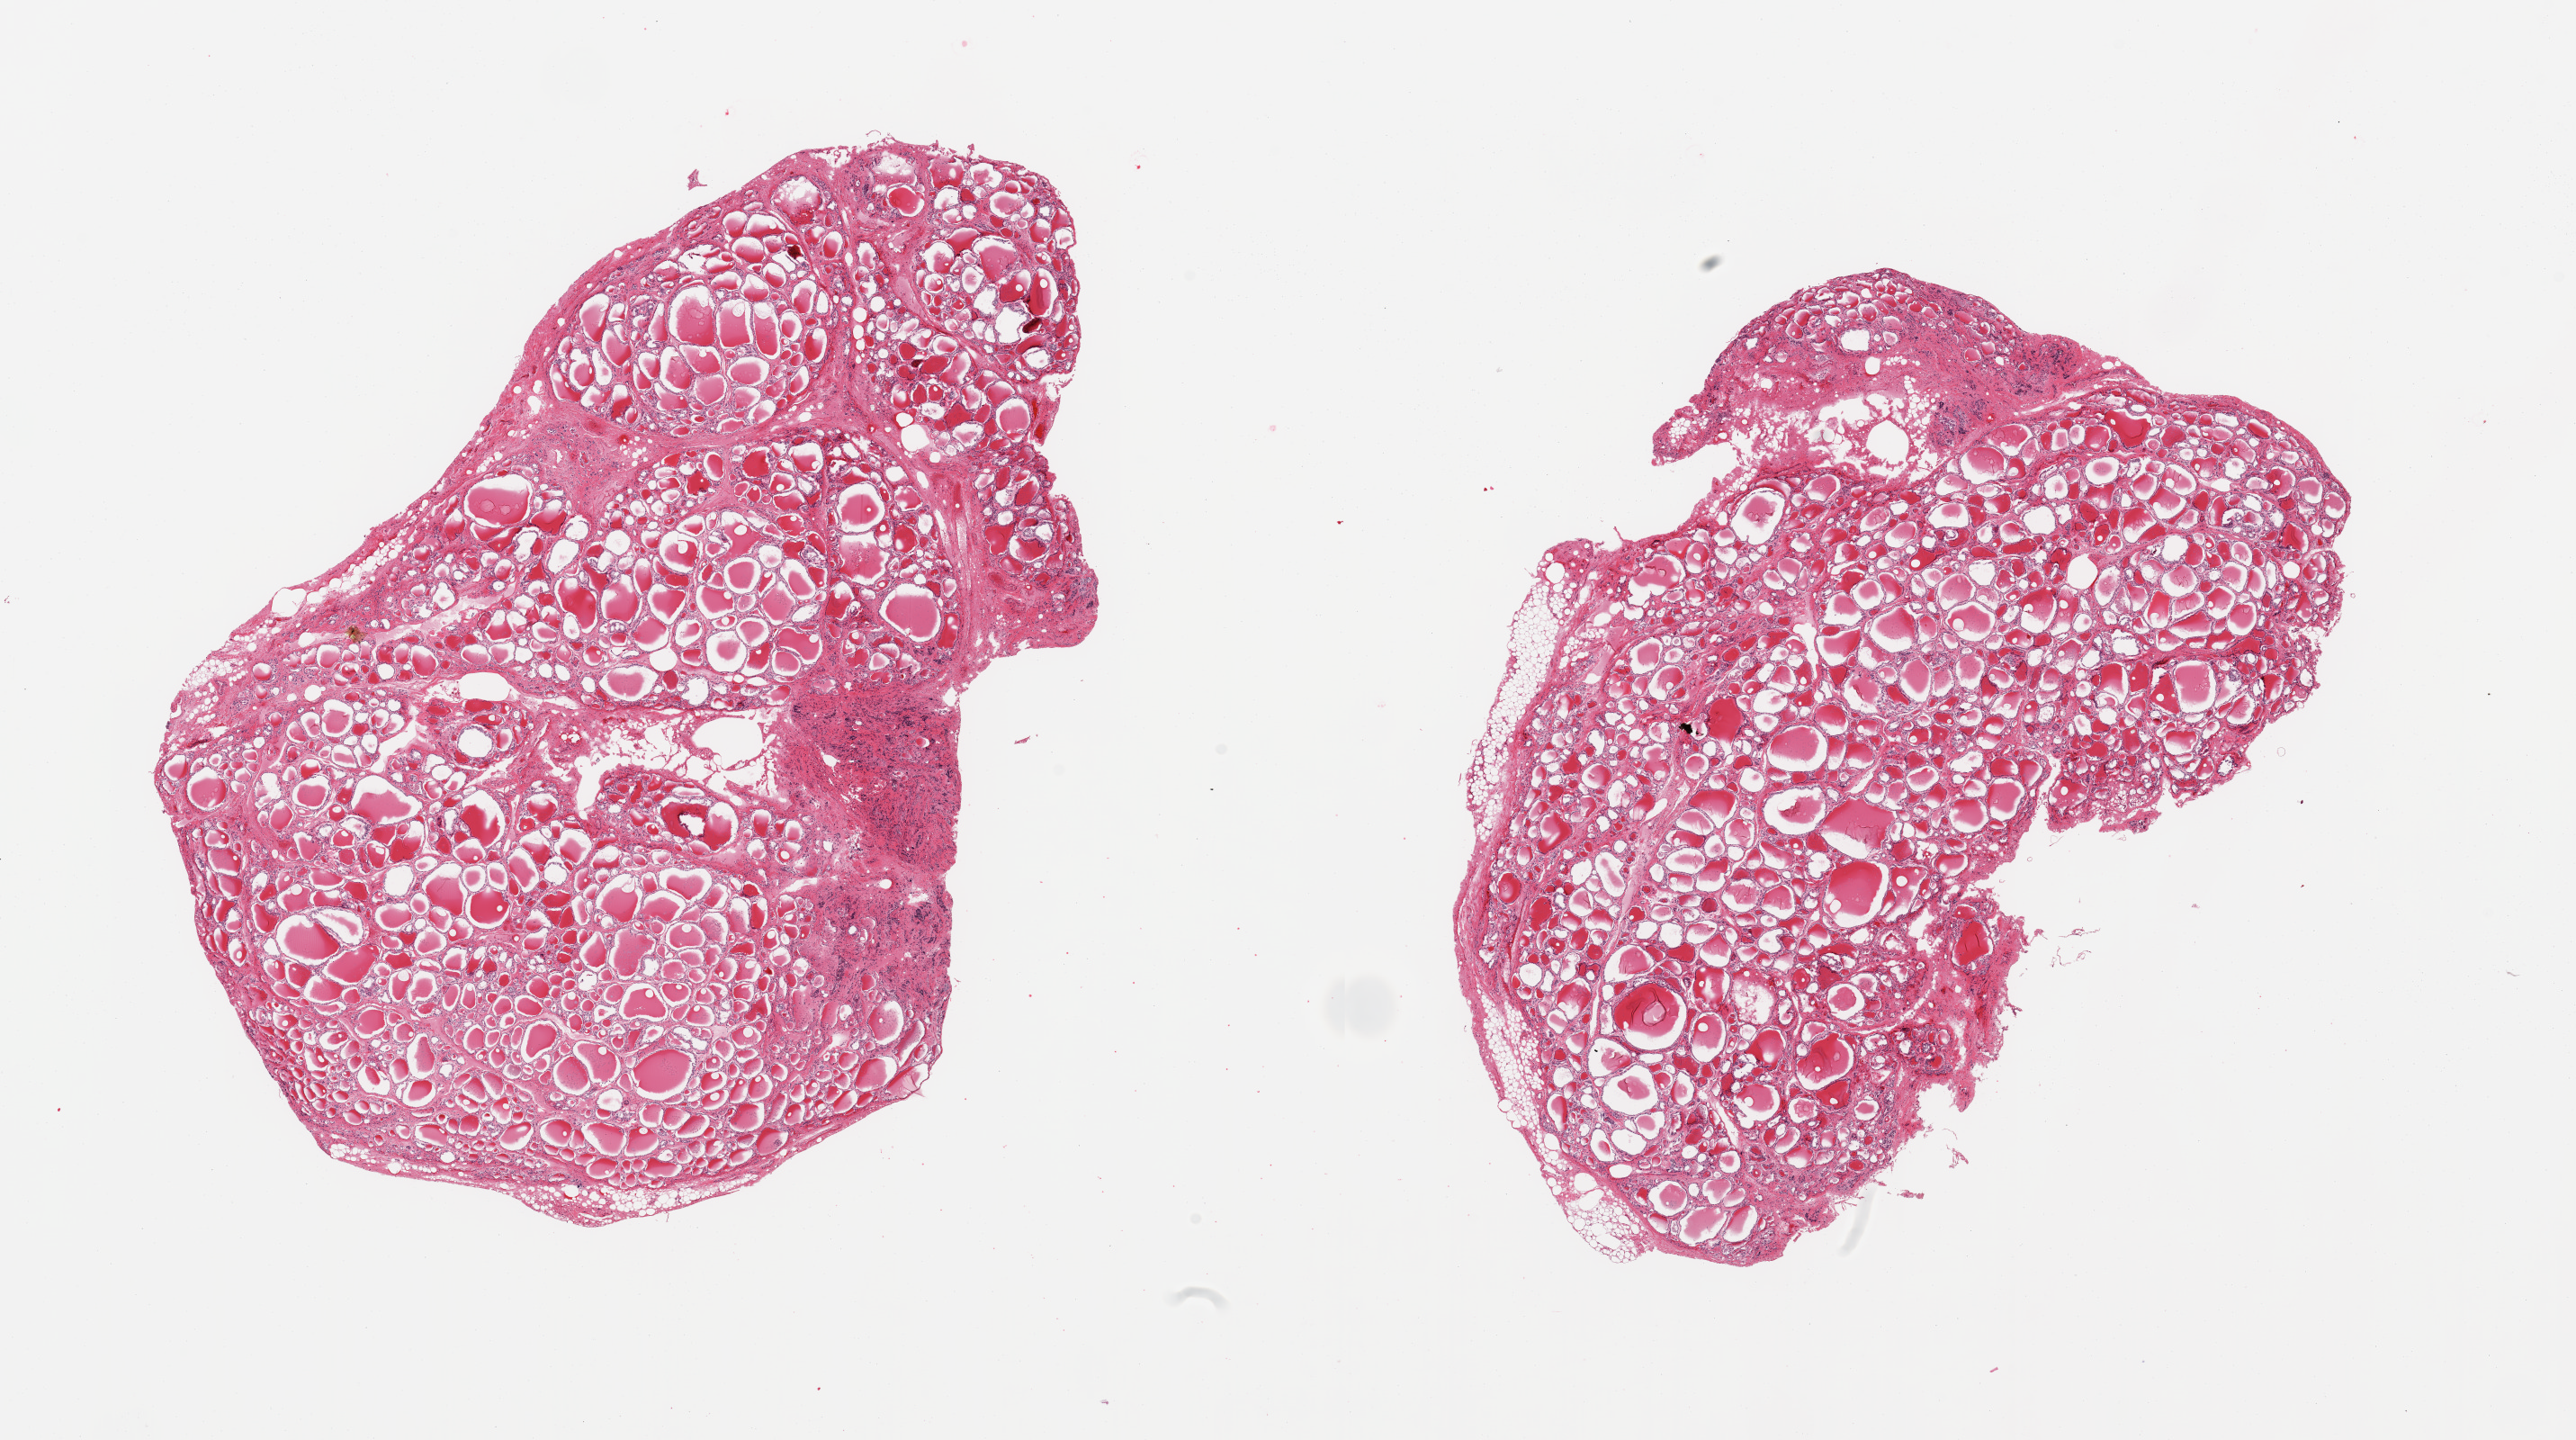
Whole-slide image, H&E stain, a low-resolution overview of the entire scanned area, about 22.6 x 12.7 mm (slide scanned at 20x). PAXgene-fixed, paraffin-embedded tissue. Section of thyroid (target tissue). Donor tissue sample.
Reviewer comment on this tissue sample: 2 pieces, no abnormalities.